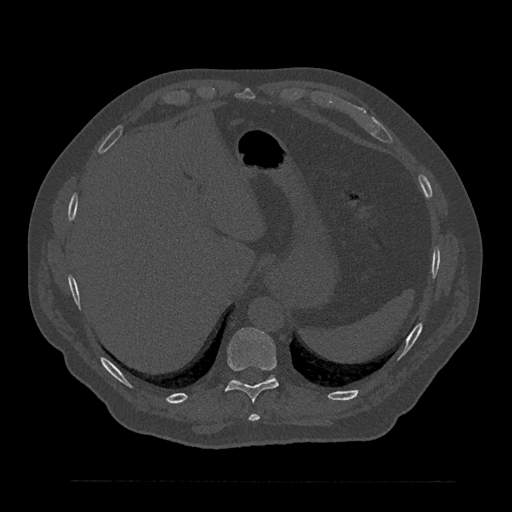
CT including the spine, one axial slice; slice 341 of 797 in the series (ordered by position); reconstruction kernel Br40s/3; 120 kVp; bone window (W 1800 / L 400 HU); 0.5 mm slice thickness; 512 × 512 image matrix, field of view 430 × 430 mm. Patient: male, 61 years. From the clinical record (not read from this slice): primary cancer: prostate.
Outlined on this slice (semi-automatic segmentation, software-assisted and operator-edited):
- T10 vertebra: bounding box (x1, y1, x2, y2) in pixels: (225, 328, 279, 403)
- T9 vertebra: (249, 413, 260, 421)